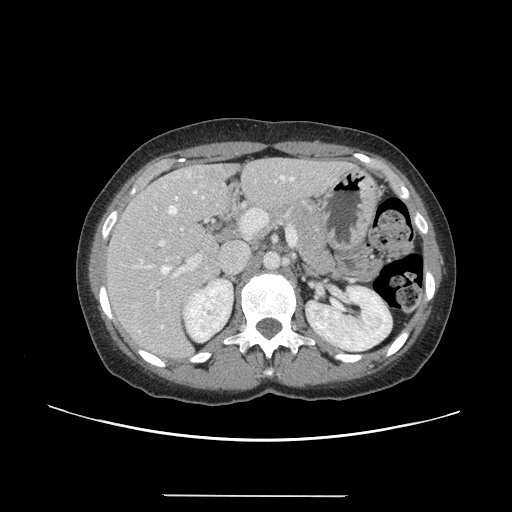
Contrast-enhanced abdominal CT, one axial slice. Slice 80 of 144 in the series (ordered by position). 120 kVp. Intravenous contrast given. Soft-tissue window (W 400 / L 40 HU). 512 × 512 image matrix, field of view 380 × 380 mm. Female patient, age 53 years. Case-level facts recorded for this patient, not image findings: diagnosis: colorectal cancer liver metastases, imaged before liver resection; multiple liver metastases: yes; largest metastasis: 1.1 cm; disease in both lobes: no.
Outlined on this slice (outlined manually by an expert reader):
- hepatic veins: bounding box [x1, y1, x2, y2] px = [161, 175, 293, 327]
- liver: [107, 159, 345, 359]
- planned liver remnant (the part of the liver to remain after resection): [108, 158, 316, 299]
- portal vein (with intrahepatic branches): [136, 205, 297, 297]